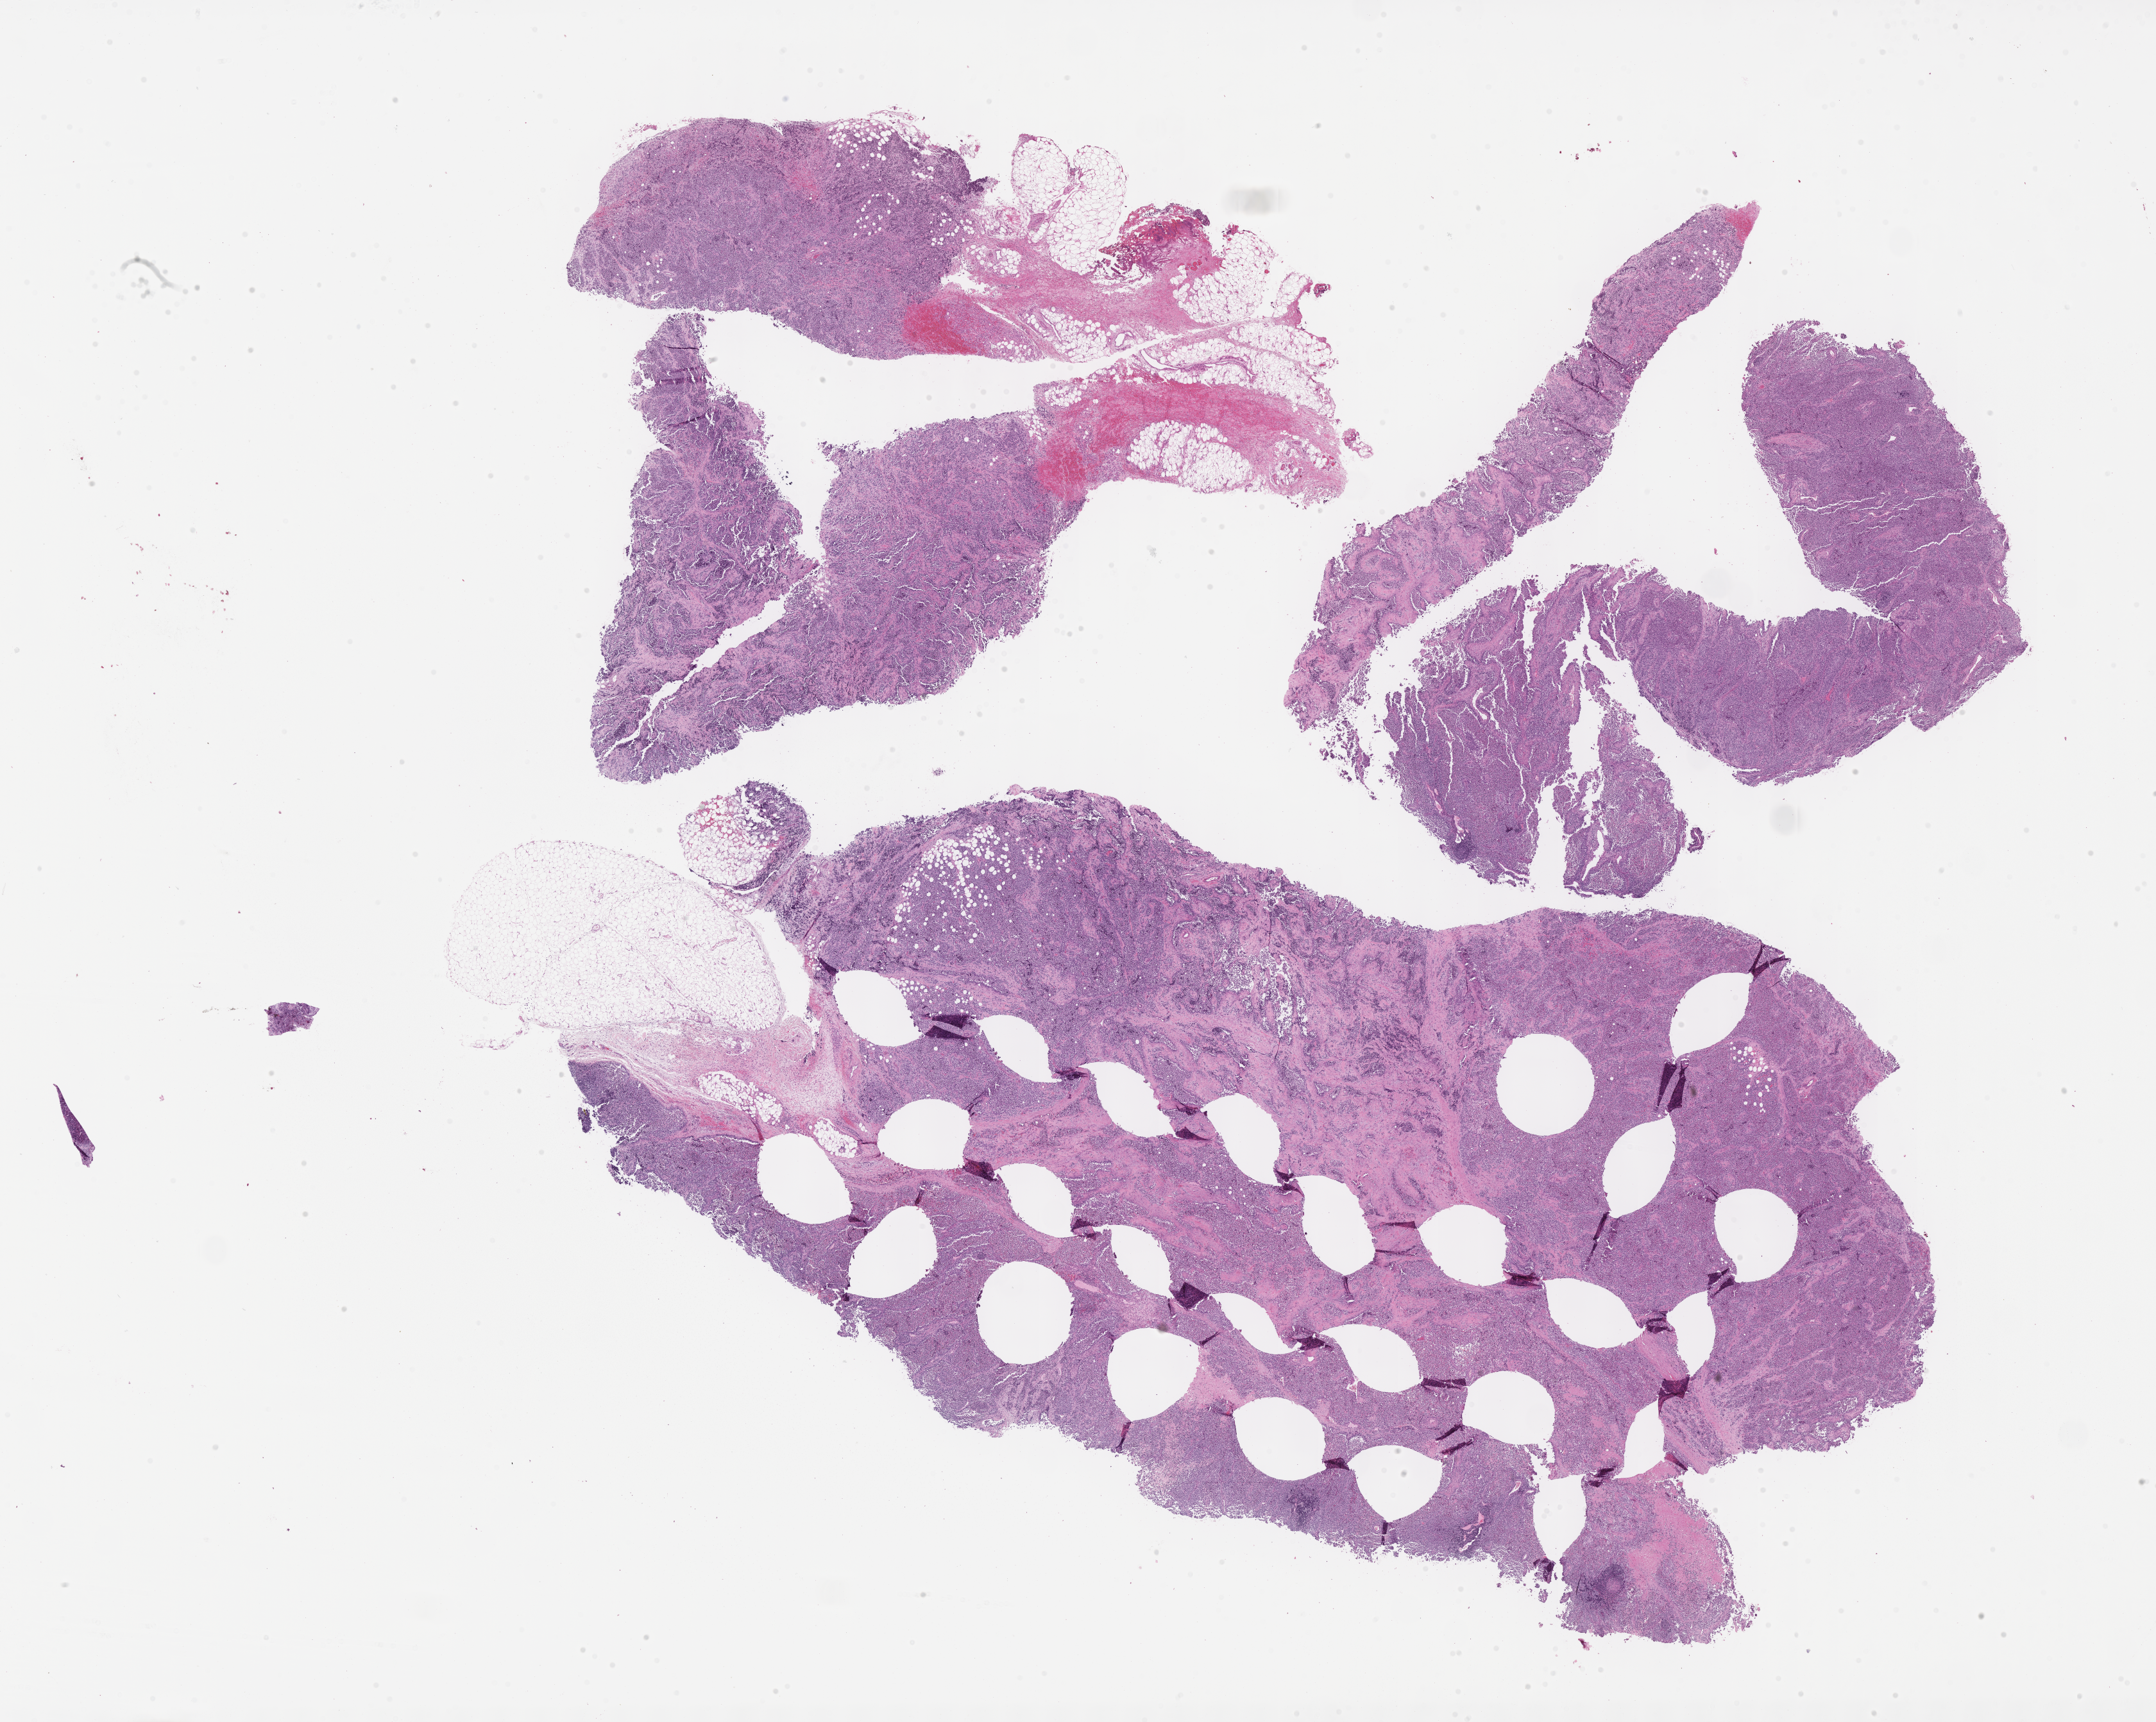
Whole-slide image, hematoxylin and eosin (H&E) stain of tumor tissue, a low-resolution overview of the entire scanned area, about 27.2 x 21.7 mm; FFPE section; site: soft tissue, hand-left. Female patient, age at diagnosis 3.6 years.
Stage (as recorded): 4. Diagnosis: rhabdomyosarcoma; histological classification: alveolar rhabdomyosarcoma.